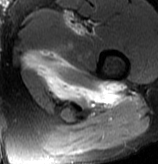
MRI of an extremity soft-tissue mass, one axial slice; position 69 of 70 along the scan axis; T2-weighted fat-saturated; MR volume resampled by the dataset authors to the PET/CT grid (not the native acquisition matrix); 3.27 mm slice thickness; 158 × 164 image matrix, field of view 154 × 160 mm. Male patient. From the clinical record (not read from this slice): histological type: extraskeletal osteosarcoma; grade: high; site of the primary tumour: left adductur.
Annotated regions visible in this slice (expert contour drawn on MRI and transferred to this co-registered scan by the dataset authors):
- gross tumour volume (mass): box from (x=36, y=12) to (x=126, y=109) px